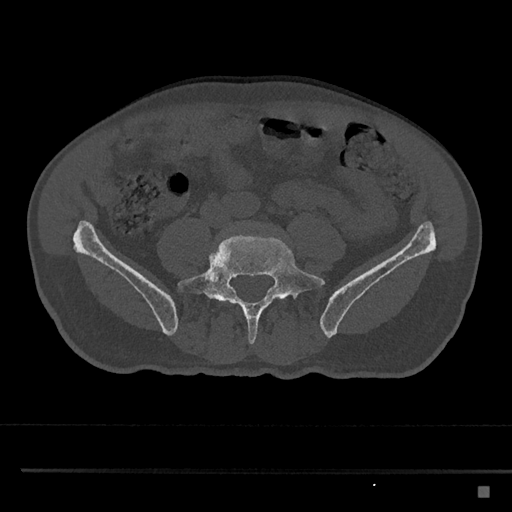
CT including the spine, one axial slice. Position 589 of 797 along the scan axis. Reconstruction kernel Br40s/3. Bone window (W 1800 / L 400 HU). 512 × 512 image matrix. Male patient, age 59 years. Case-level facts recorded for this patient, not image findings: primary cancer: prostate.
Structures marked on this image (semi-automatic segmentation, software-assisted and operator-edited):
- L5 vertebra: box from (x=178, y=233) to (x=325, y=345) px